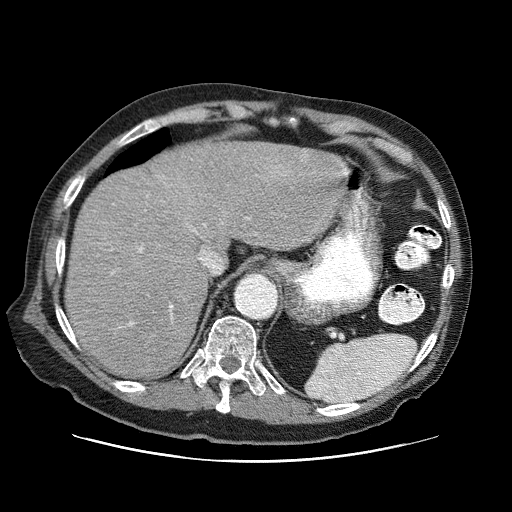
Contrast-enhanced abdominal CT (liver protocol), one axial slice; position 57 of 87 along the scan axis; reconstruction kernel STANDARD; 120 kVp; one of 3 acquisitions stored at this slice position; soft-tissue window (W 400 / L 40 HU); 2.5 mm slice thickness; 512 × 512 image matrix. From the clinical record (not read from this slice): diagnosis: hepatocellular carcinoma (patient treated with transarterial chemoembolisation; whether this scan precedes or follows treatment is not stated here); TNM stage (as recorded): Stage-IIIA; Child-Pugh class: A; tumour differentiation: well differentiated; tumour nodularity: multinodular.
Structures marked on this image (semi-automatically segmented with operator editing):
- abdominal aorta: bounding box (x1, y1, x2, y2) in pixels: (238, 276, 275, 318)
- liver parenchyma outside the tumour (the mass and vessels are separate outlines, so this box may not span the whole liver): (64, 142, 348, 378)
- liver vessels: (112, 169, 346, 325)